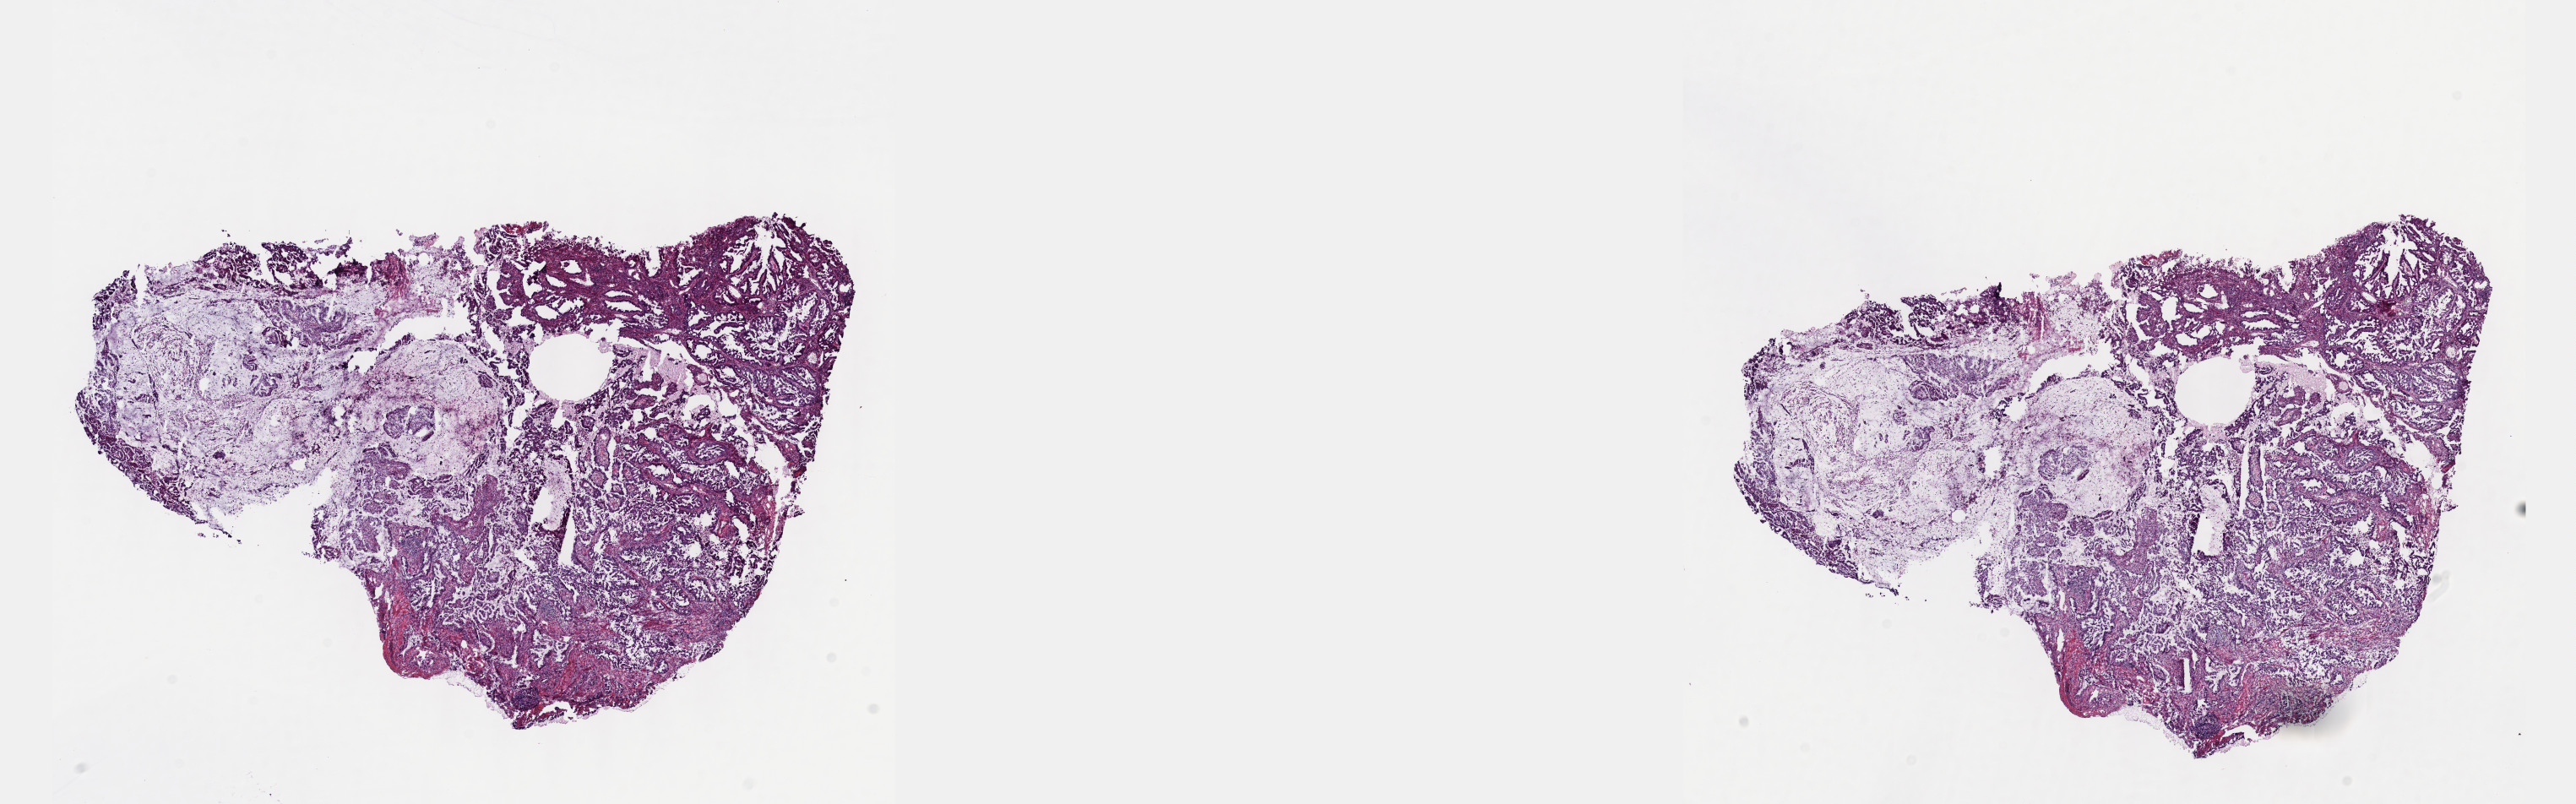
Digitized H&E-stained tissue section (whole slide) — shown as a low-resolution overview of the whole scanned area (about 24.6 x 7.7 mm, from a 40x scan); frozen section from the top of the tissue portion; cervix, primary tumour sample. Patient: female, age at initial diagnosis 50 years. Histologic grade: G2 (moderately differentiated). Slide review estimates, as recorded: tumour cells 100%, tumour nuclei 70%, normal cells 0%, stromal cells 0%, necrosis 0%. Infiltration values recorded for this section: lymphocyte infiltration 5%, monocyte infiltration 1%, neutrophil infiltration 2%.
Pathologic diagnosis: Mucinous adenocarcinoma, endocervical type. FIGO stage: IIB.